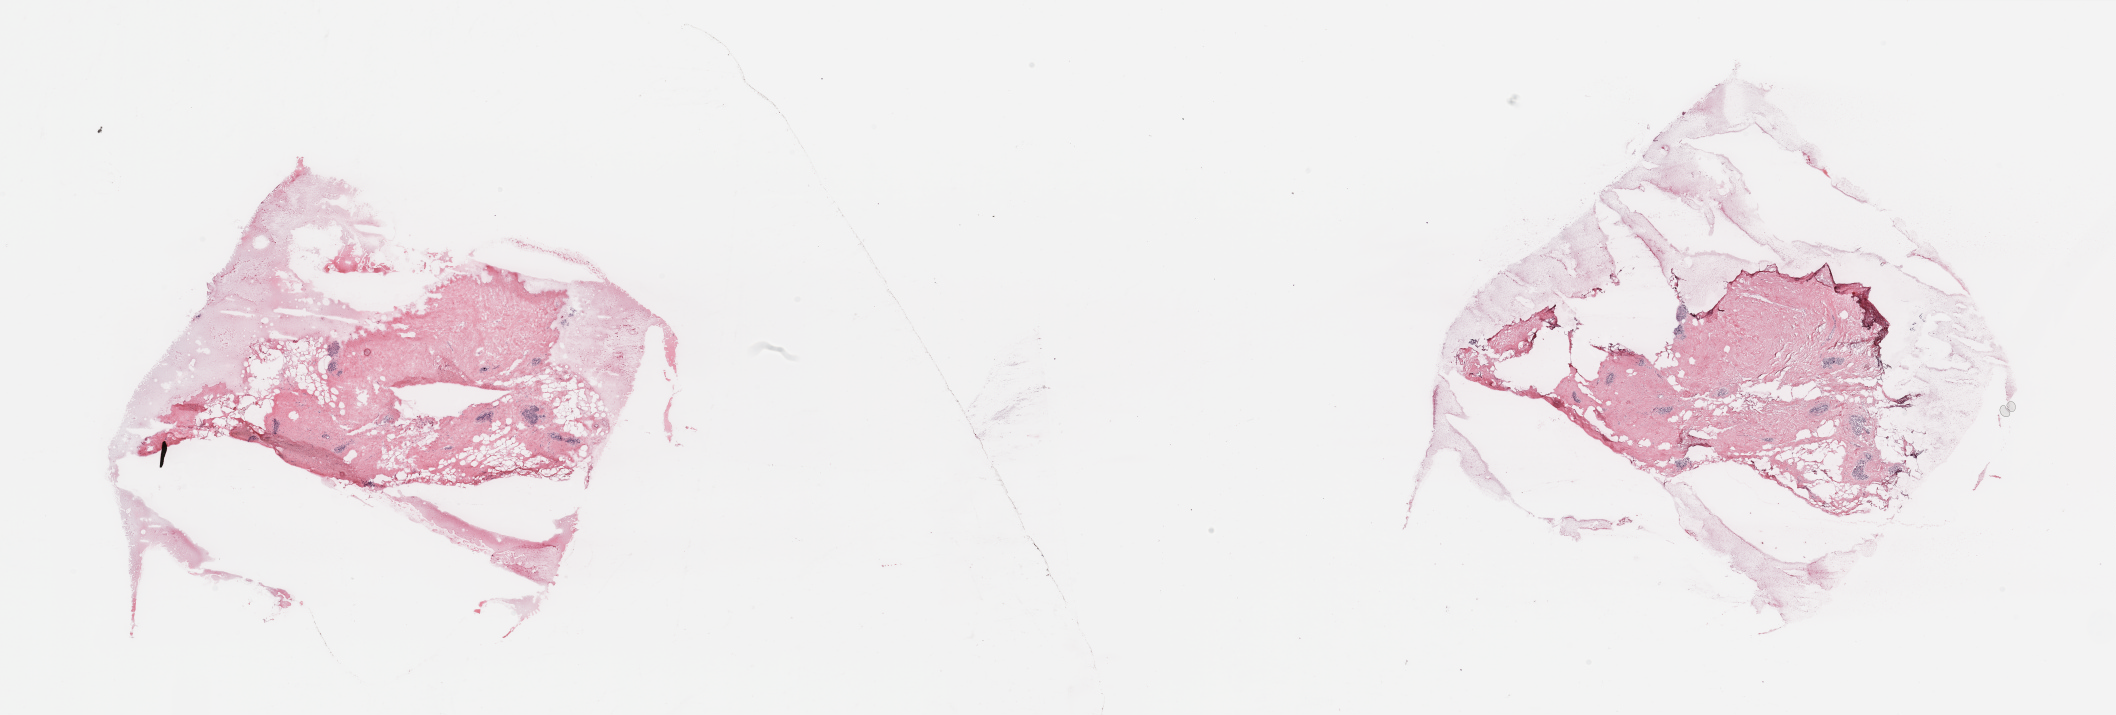
Digitized Hematoxylin and eosin (H&E) stained tissue section (whole slide), shown as a low-resolution overview of the whole scanned area (about 33.5 x 11.3 mm); breast, tissue type not recorded.
* patient diagnosis (cohort enrolment): breast cancer (breast)